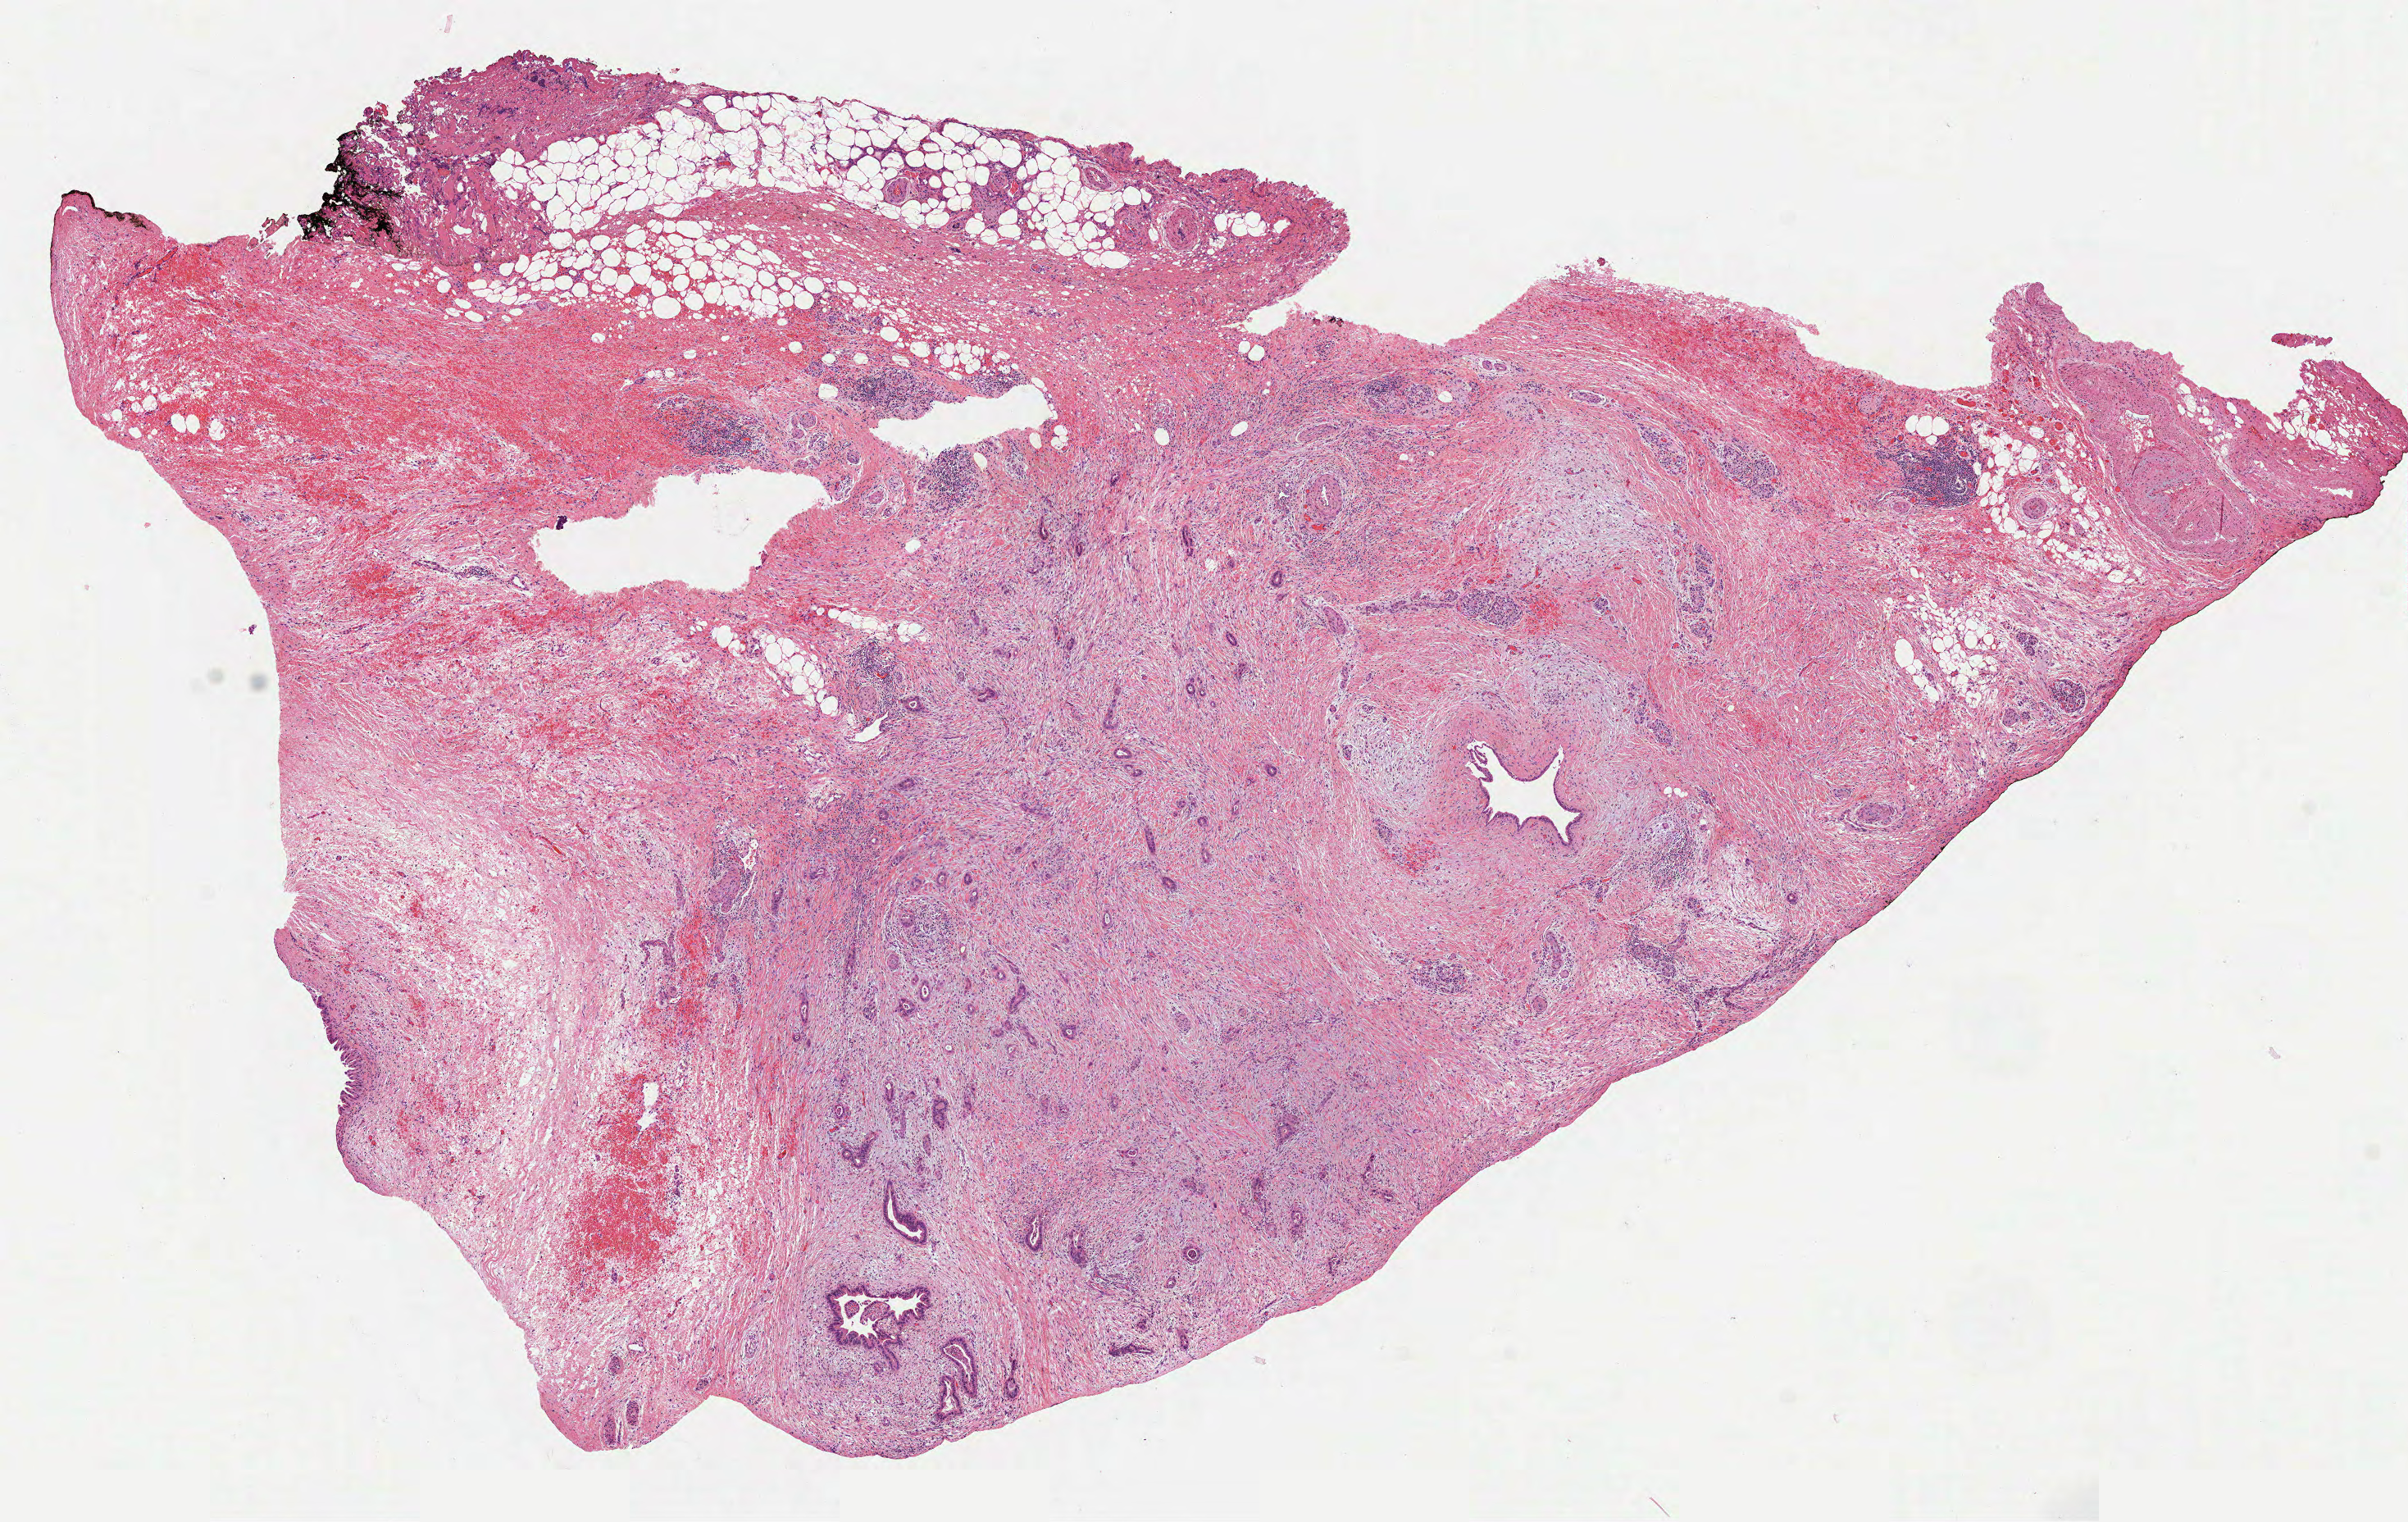
H&E whole-slide image — shown as a low-resolution overview of the whole scanned area (about 11.8 x 7.5 mm), formalin-fixed paraffin-embedded (FFPE) diagnostic section, pancreas, primary tumour sample. Male, age 66 years at initial diagnosis. Histologic grade: G2 (moderately differentiated).
- AJCC pathologic stage: IIB (7th edition)
- lymph nodes positive (case pathology): 2 of 19 examined
- diagnosis: Infiltrating duct carcinoma, NOS (head of pancreas)